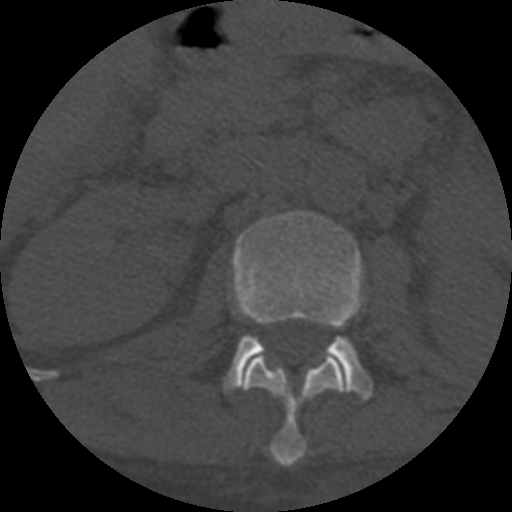
CT including the spine, one axial slice. Position 272 of 708 along the scan axis. 120 kVp. One of 3 acquisitions stored at this slice position. Bone window (W 1800 / L 400 HU). 1.25 mm slice thickness. 512 × 512 image matrix. Patient age 55 years. From the clinical record (not read from this slice): primary cancer: colon; vertebrae with lytic lesions (as recorded): T12, L1, L5.
Structures marked on this image (semi-automatic segmentation, software-assisted and operator-edited):
- L1 vertebra: box from (x=243, y=351) to (x=348, y=467) px
- L2 vertebra: (x=226, y=211)–(x=373, y=399)